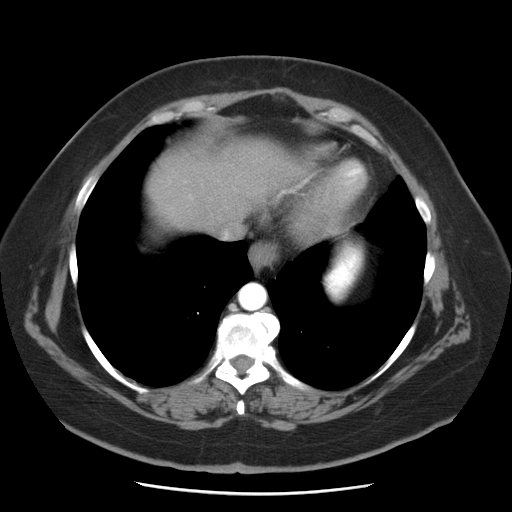
Contrast-enhanced abdominal CT, one axial slice. Slice 43 of 55 in the series (ordered by position). Reconstruction kernel STANDARD. 120 kVp. Intravenous contrast given. Soft-tissue window (W 400 / L 40 HU). 5 mm slice thickness. 512 × 512 image matrix. Female patient, age 52 years. Case-level facts recorded for this patient, not image findings: diagnosis: colorectal cancer liver metastases, imaged before liver resection; multiple liver metastases: yes; largest metastasis: 2.5 cm; disease in both lobes: yes.
Structures marked on this image (expert manual segmentation):
- liver: bounding box [x1, y1, x2, y2] px = [144, 135, 308, 234]